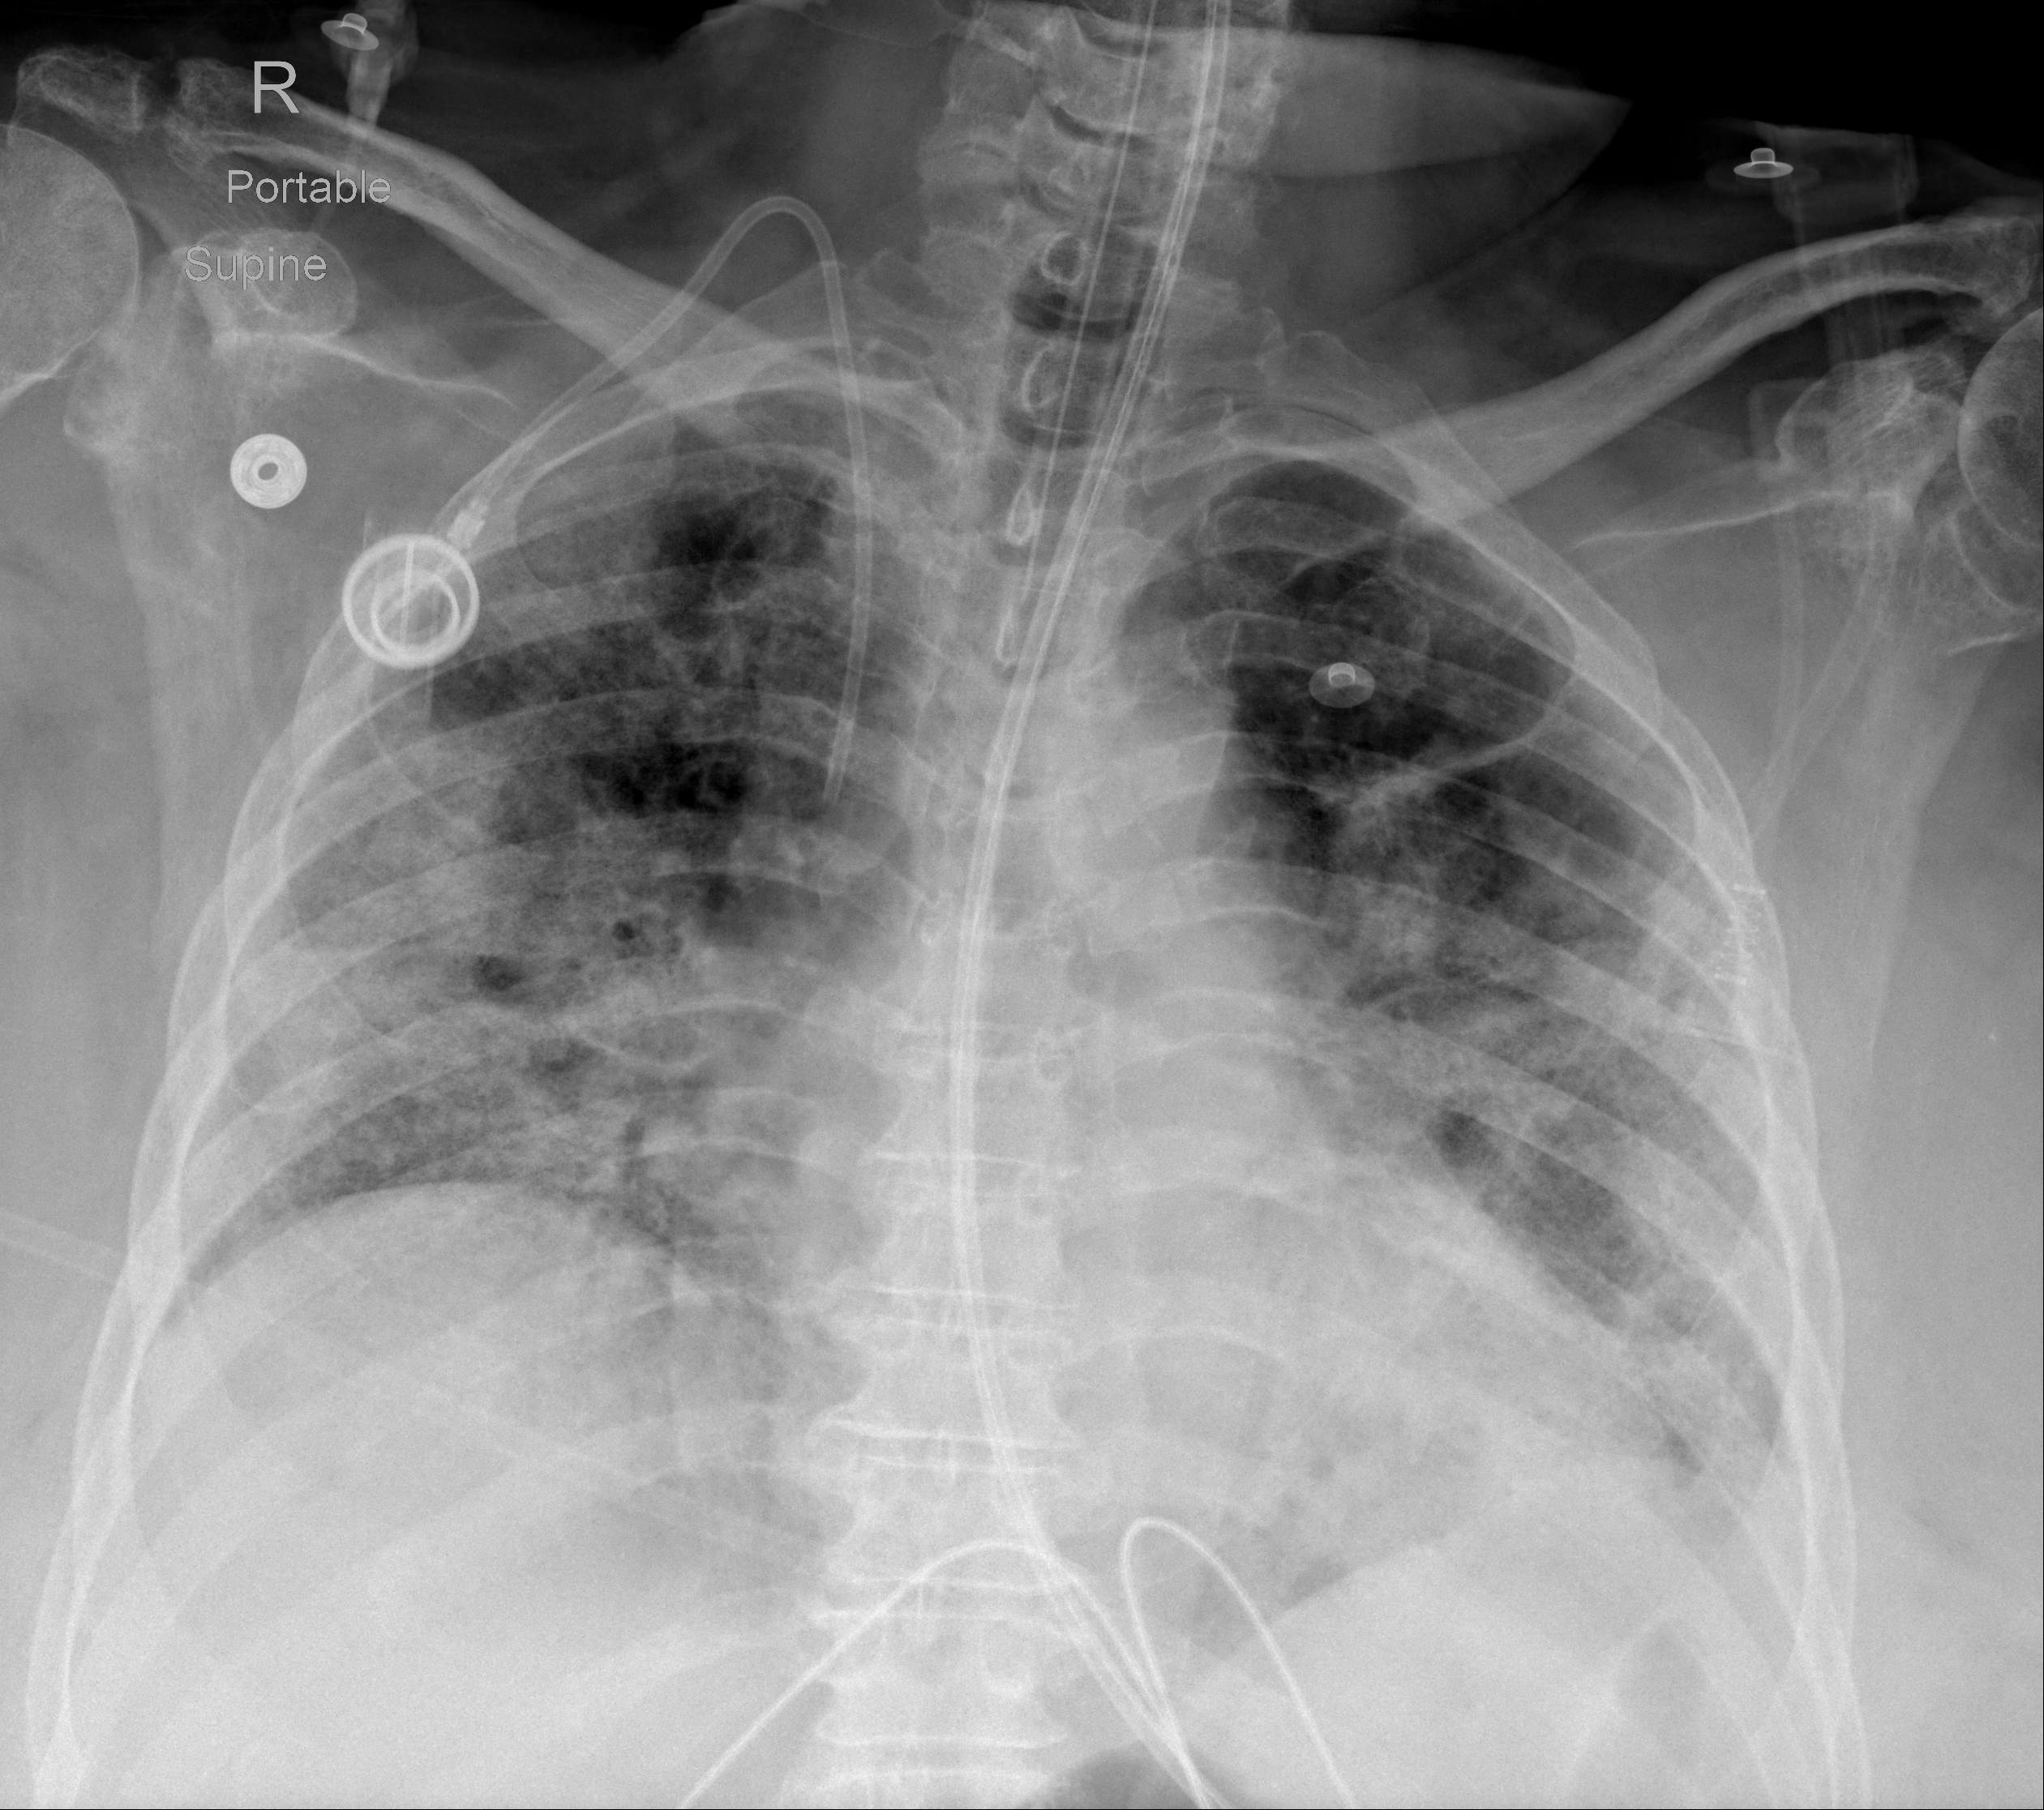
Portable chest radiograph, AP projection. Female patient, age 76 years; imaged 5 days after the COVID-19 diagnosis.
Radiologist's key findings for this exam: Stable hazy ill-defined airspace opacities throughout both lungs.